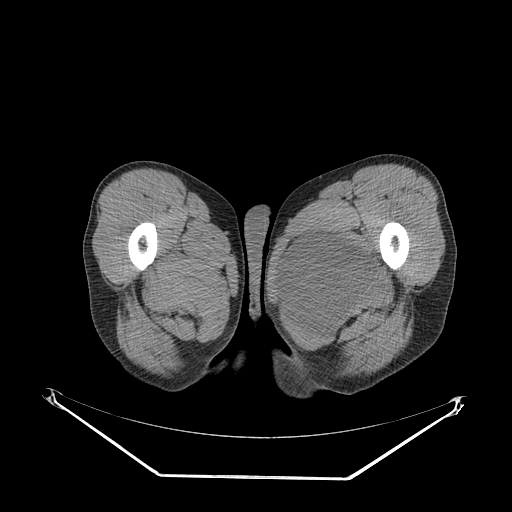
CT of an extremity soft-tissue mass (from a PET/CT study), one axial slice. Position 33 of 267 along the scan axis. Reconstruction kernel SOFT. Soft-tissue window (W 400 / L 40 HU). 512 × 512 image matrix, field of view 500 × 500 mm. Male patient. From the clinical record (not read from this slice): histological type: pleiomorphic liposarcoma; grade: high; site of the primary tumour: left thigh.
Annotated regions visible in this slice (expert contour drawn on MRI and transferred to this co-registered scan by the dataset authors):
- gross tumour volume including surrounding oedema: bounding box (x1, y1, x2, y2) in pixels: (283, 230, 375, 325)
- gross tumour volume (mass): (283, 231, 373, 316)